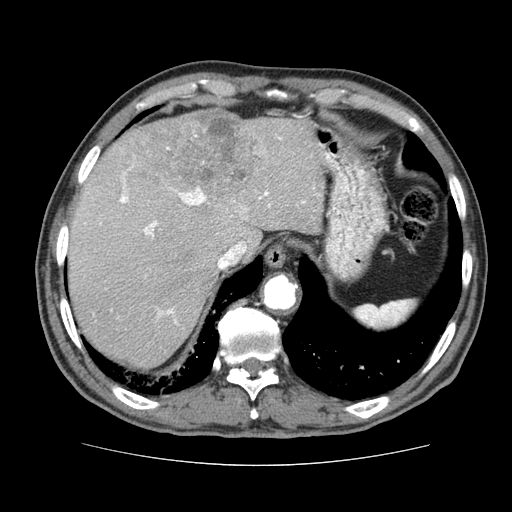
Contrast-enhanced abdominal CT (liver protocol), one axial slice. Position 60 of 79 along the scan axis. Reconstruction kernel STANDARD. 120 kVp. Soft-tissue window (W 400 / L 40 HU). 512 × 512 image matrix. From the clinical record (not read from this slice): diagnosis: hepatocellular carcinoma (patient treated with transarterial chemoembolisation; whether this scan precedes or follows treatment is not stated here); TNM stage (as recorded): Stage-I; Child-Pugh class: A.
Structures marked on this image (semi-automatic segmentation, software-assisted and operator-edited):
- liver parenchyma outside the tumour (the mass and vessels are separate outlines, so this box may not span the whole liver): bounding box (x1, y1, x2, y2) in pixels: (68, 114, 326, 368)
- mass: (128, 108, 269, 206)
- liver vessels: (120, 137, 321, 324)